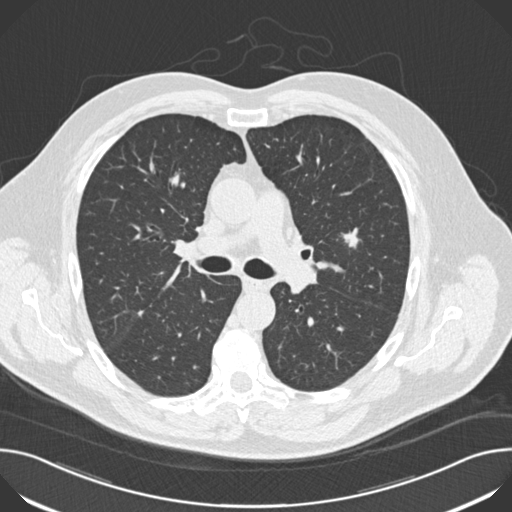
Low-dose screening chest CT, one axial slice. Slice 108 of 174 in the series (ordered by position). 120 kVp. Lung window (W 1500 / L -600 HU). 2 mm slice thickness. 512 × 512 image matrix, field of view 380 × 380 mm.
Annotated regions visible in this slice (manually delineated by an expert):
- lesion 1 (tumor, upper lobe of left lung): bounding box [x1, y1, x2, y2] px = [343, 228, 359, 247]